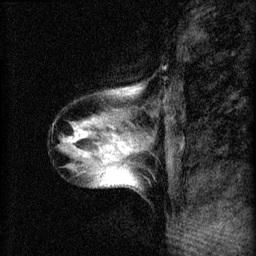
Breast MRI (dynamic contrast-enhanced), one sagittal slice. 3 images stored at this slice position (order not interpretable as contrast timing). 1.5 T. TE 4.2 ms, TR 8.2 ms. 2 mm slice thickness. 256 × 256 image matrix, field of view 180 × 180 mm. Patient: female, 40 years.
Structures marked on this image (semi-automatic segmentation, software-assisted and operator-edited):
- analysis volume of interest (the breast-tissue region the enhancement analysis was run in; not a lesion): bounding box <57,80,165,191> (left, top, right, bottom; pixels)
- tumour enhancement mask (voxels above the 70 % enhancement threshold inside the analysis volume of interest): <73,132,132,151>